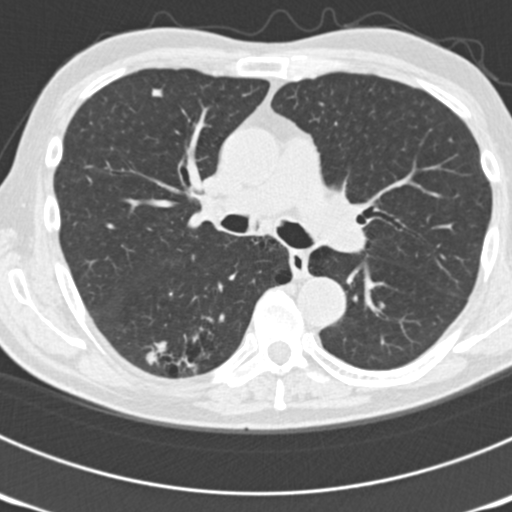
Low-dose screening chest CT, axial slice. Third screening round (two years after baseline). Lung window (W 1500 / L -600 HU). Standard (soft-tissue) reconstruction kernel (B30f). Male, age 70 years at enrolment. Current smoker at enrolment.
- Expert reader's lesion annotation, bounding box <143,311,237,386> (left, top, right, bottom; pixels).
- The screening reader recorded 3 non-calcified nodules or masses ≥4 mm on this exam (right upper lobe, left upper lobe, right lower lobe); which of them this box marks is not recorded.